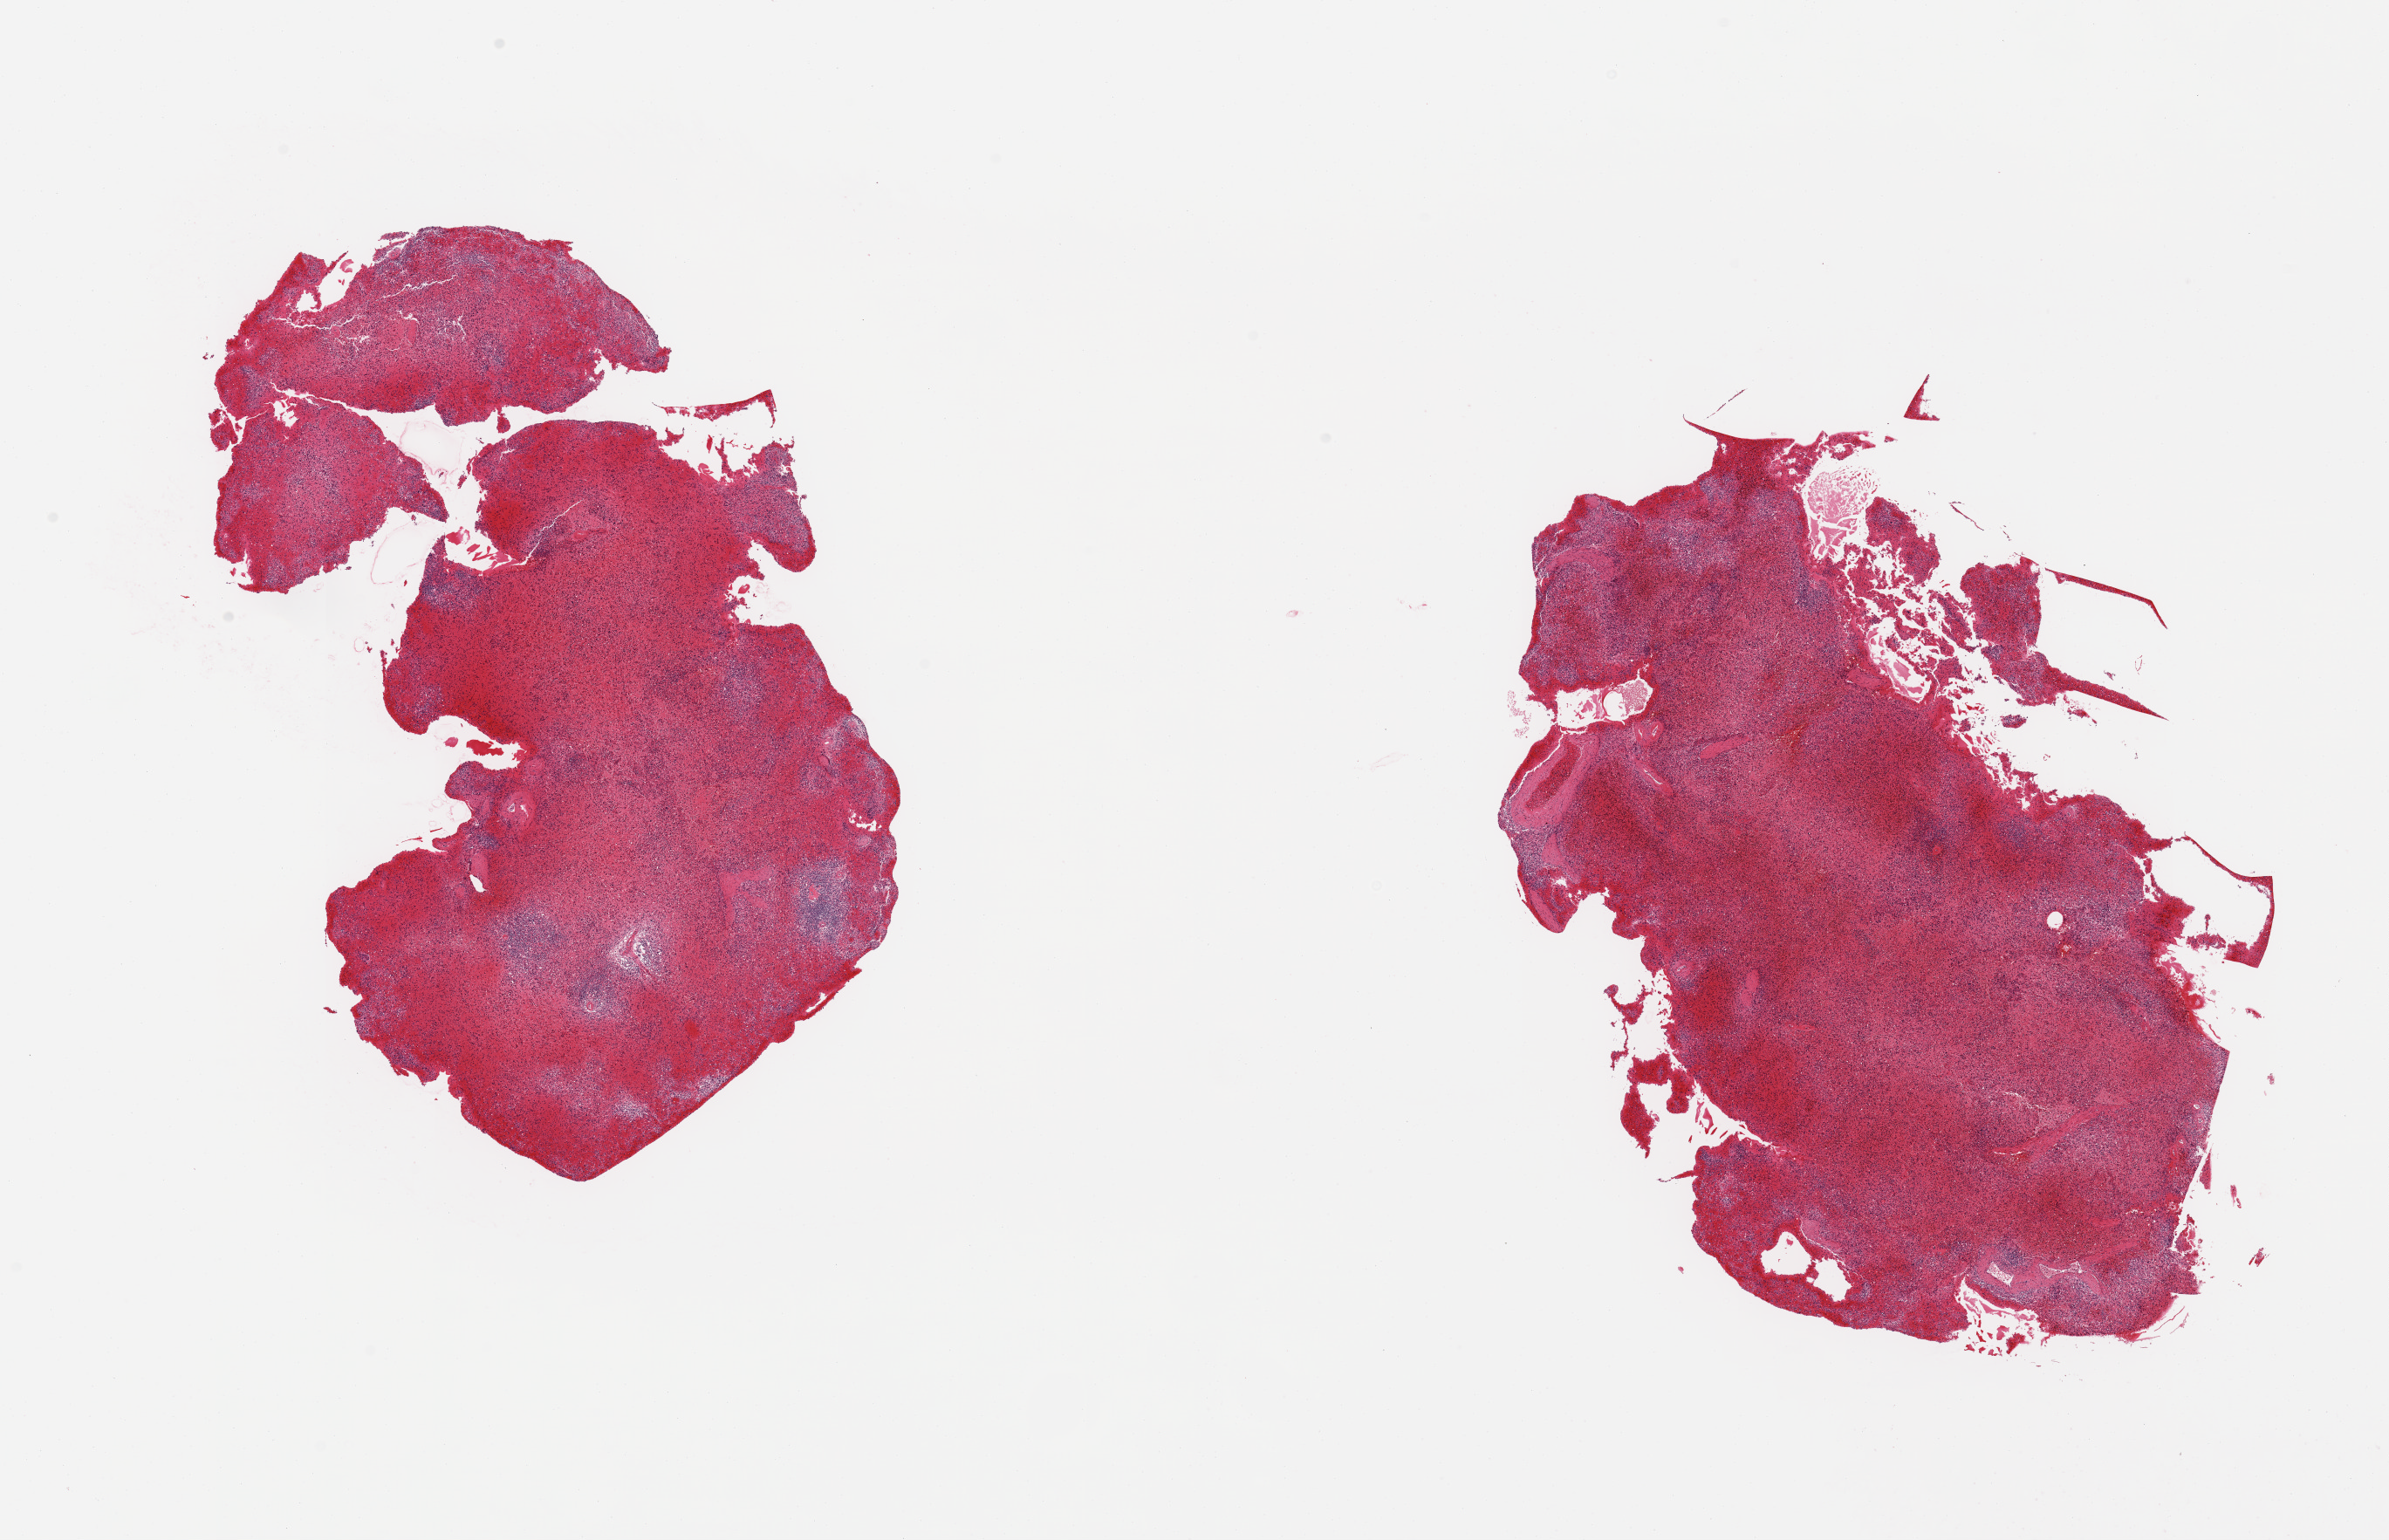
Whole-slide image, haematoxylin and eosin stain, shown as a low-resolution overview of the whole scanned area (about 21.7 x 14.0 mm). PAXgene-fixed paraffin-embedded (PFPE) section. Target tissue: spleen. Donor tissue sample. Donor sex: male.
Pathologist's review note for this sample: 2 pieces; severe vascular congestion.